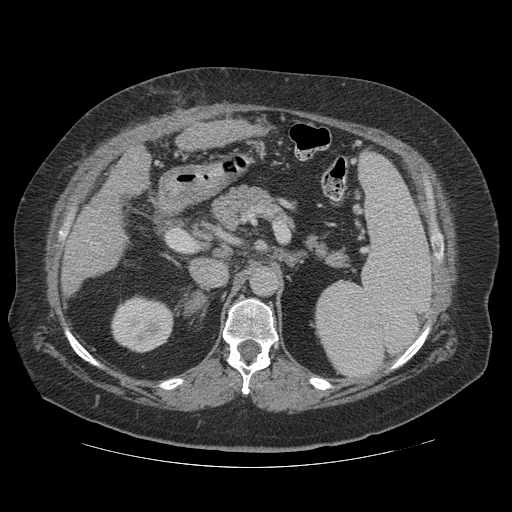
Contrast-enhanced abdominal CT (liver protocol), one axial slice. Slice 63 of 121 in the series (ordered by position). Reconstruction kernel STANDARD. 140 kVp. Soft-tissue window (W 400 / L 40 HU). 512 × 512 image matrix. From the clinical record (not read from this slice): diagnosis: hepatocellular carcinoma (patient treated with transarterial chemoembolisation; whether this scan precedes or follows treatment is not stated here); TNM stage (as recorded): Stage-IIIA; Child-Pugh class: A; tumour differentiation: well differentiated.
Outlined on this slice (semi-automatic segmentation, software-assisted and operator-edited):
- liver parenchyma outside the tumour (the mass and vessels are separate outlines, so this box may not span the whole liver): box from (x=80, y=120) to (x=263, y=242) px
- liver vessels: (x=92, y=211)–(x=94, y=225)